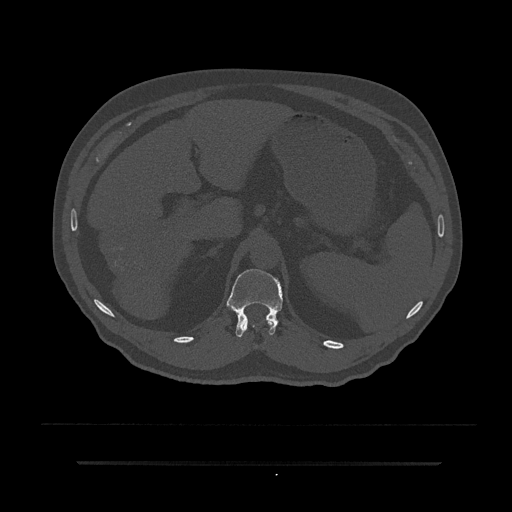
CT including the spine, one axial slice. Slice 230 of 797 in the series (ordered by position). Reconstruction kernel Br40s/3. 120 kVp. Bone window (W 1800 / L 400 HU). 0.5 mm slice thickness. 512 × 512 image matrix, field of view 464 × 464 mm. Male patient, age 59 years. Case-level facts recorded for this patient, not image findings: primary cancer: bile ducts.
Annotated regions visible in this slice (semi-automatic segmentation, software-assisted and operator-edited):
- T11 vertebra: bounding box [x1, y1, x2, y2] px = [244, 320, 274, 330]
- T12 vertebra: [227, 269, 283, 337]